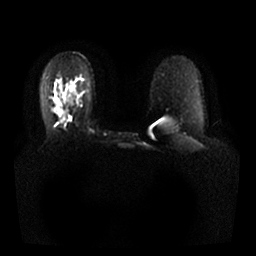
Breast MRI, one axial slice. Slice 19 of 25 in the series (ordered by position). Diffusion-weighted series; image 2 of 4 stored at this slice position (different b-values; order by instance number). 1.5 T. 256 × 256 image matrix. Female patient.
Outlined on this slice (expert manual segmentation):
- tumour on diffusion-weighted imaging: box from (x=55, y=108) to (x=65, y=123) px